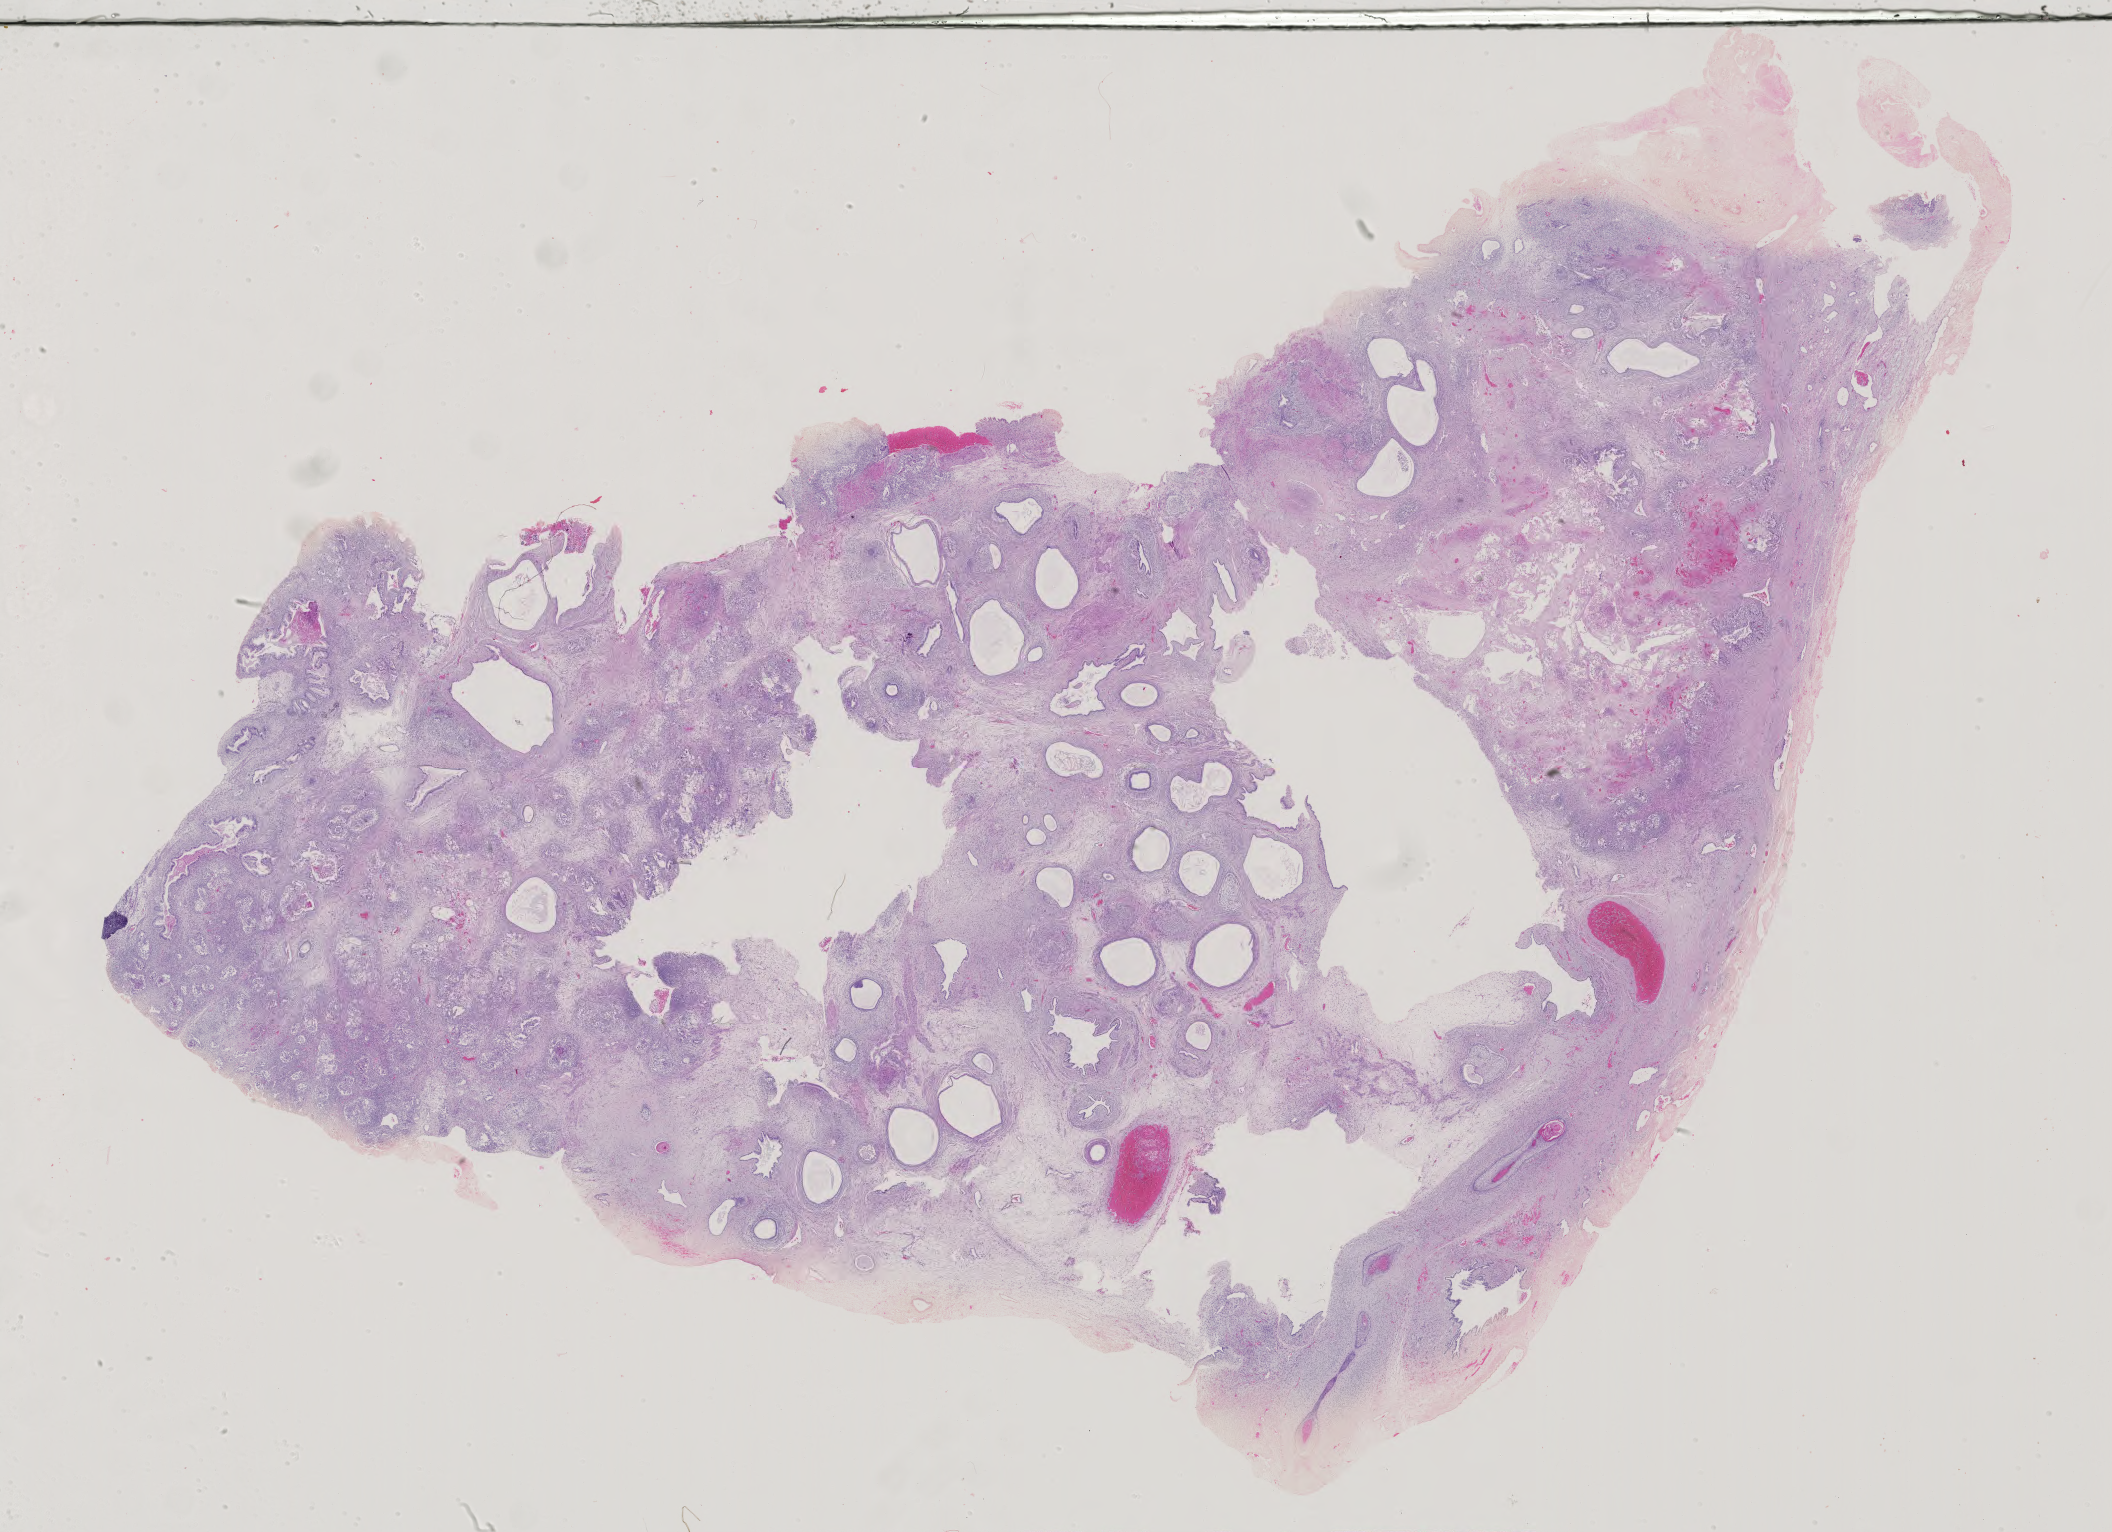
Whole-slide histology image, H&E-stained, whole scanned area (about 30.8 x 22.3 mm) shown as a low-resolution overview. FFPE section. Testis, primary tumour sample. Patient: male, age at initial diagnosis 22 years.
AJCC pathologic stage: I (4th edition). Diagnosis: Embryonal carcinoma, NOS. Laterality: left. TNM: T1 N0 M0.